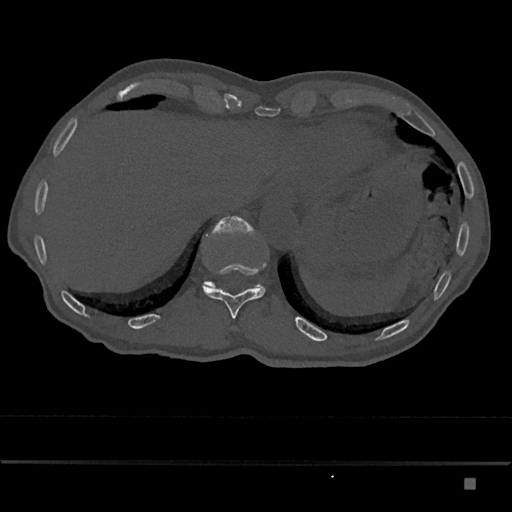
CT including the spine, one axial slice; slice 664 of 797 in the series (ordered by position); reconstruction kernel Br40s/3; 120 kVp; bone window (W 1800 / L 400 HU); 512 × 512 image matrix, field of view 390 × 390 mm. Male patient, age 72 years. From the clinical record (not read from this slice): primary cancer: prostate.
Outlined on this slice (semi-automatic segmentation, software-assisted and operator-edited):
- T11 vertebra: bounding box (x1, y1, x2, y2) in pixels: (202, 264, 266, 319)
- T12 vertebra: (203, 216, 262, 288)